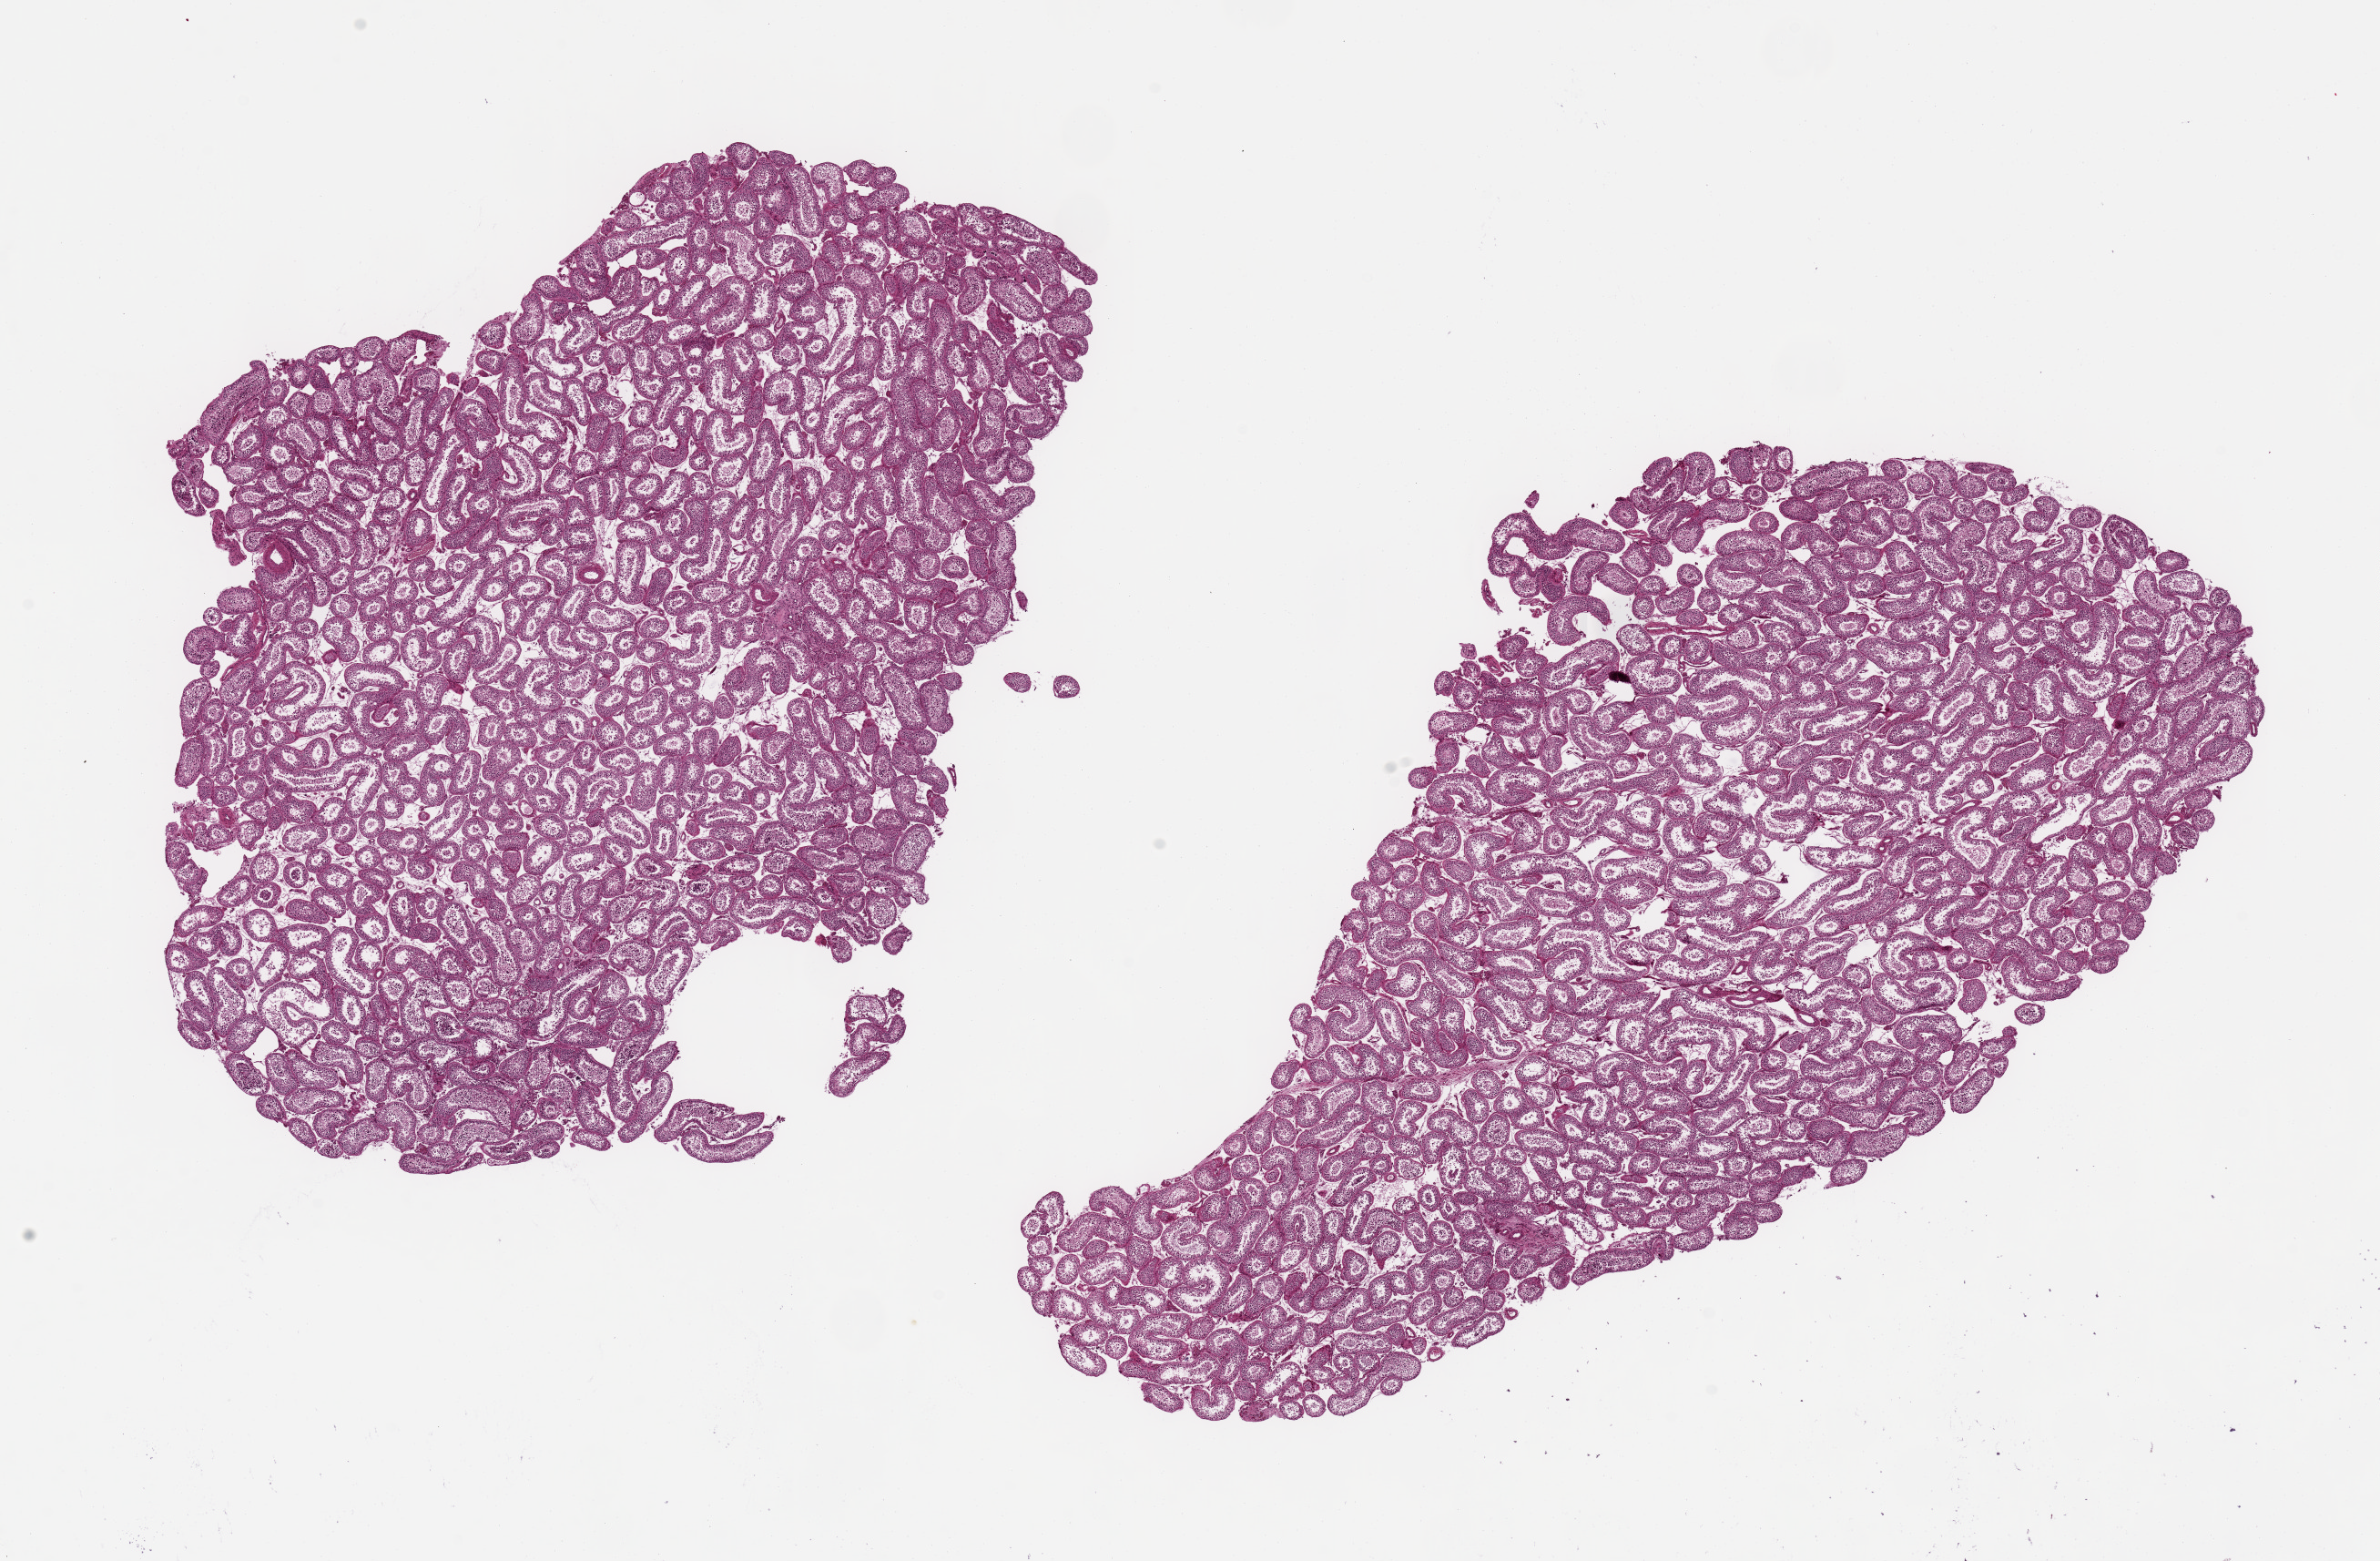
Whole-slide image, hematoxylin and eosin (H&E) stain, low-resolution overview of the scanned area, about 20.7 x 13.6 mm (acquisition: 20x scan), PAXgene-fixed, paraffin-embedded tissue, sampled site (target tissue): testis, donor tissue sample. Male donor.
* reviewer comment on this tissue sample: 2 pieces up to 10x6 mm; spermatogenesis